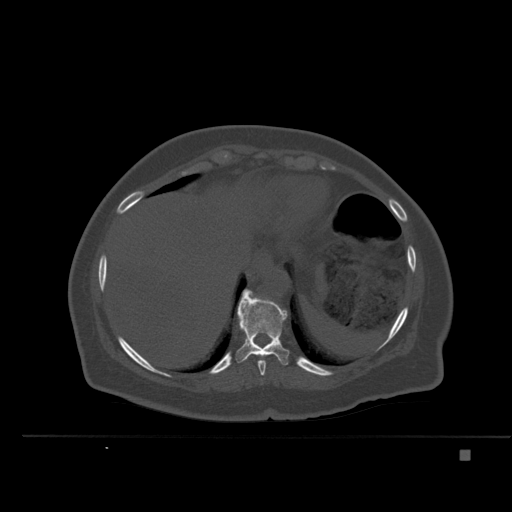
CT including the spine, one axial slice; position 285 of 477 along the scan axis; bone window (W 1800 / L 400 HU); 1.5 mm slice thickness; 512 × 512 image matrix. Female patient, age 74 years. Case-level facts recorded for this patient, not image findings: primary cancer: colon.
Structures marked on this image (semi-automatically segmented with operator editing):
- T10 vertebra: bounding box [x1, y1, x2, y2] px = [236, 293, 290, 366]
- T11 vertebra: [243, 289, 253, 295]
- T9 vertebra: [254, 354, 266, 376]